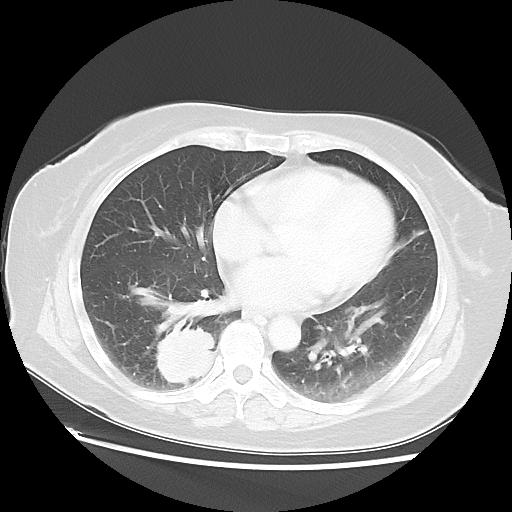
Chest CT, one axial slice; position 24 of 52 along the scan axis; 120 kVp; lung window (W 1500 / L -600 HU); 5 mm slice thickness; 512 × 512 image matrix. Patient: female, 69 years. Case-level facts recorded for this patient, not image findings: clinical TNM (as recorded): T2 N1 M1a.
Structures marked on this image (bounding box drawn by a radiologist):
- lung tumour (recorded histology: adenocarcinoma): bounding box <145,312,223,389> (left, top, right, bottom; pixels)